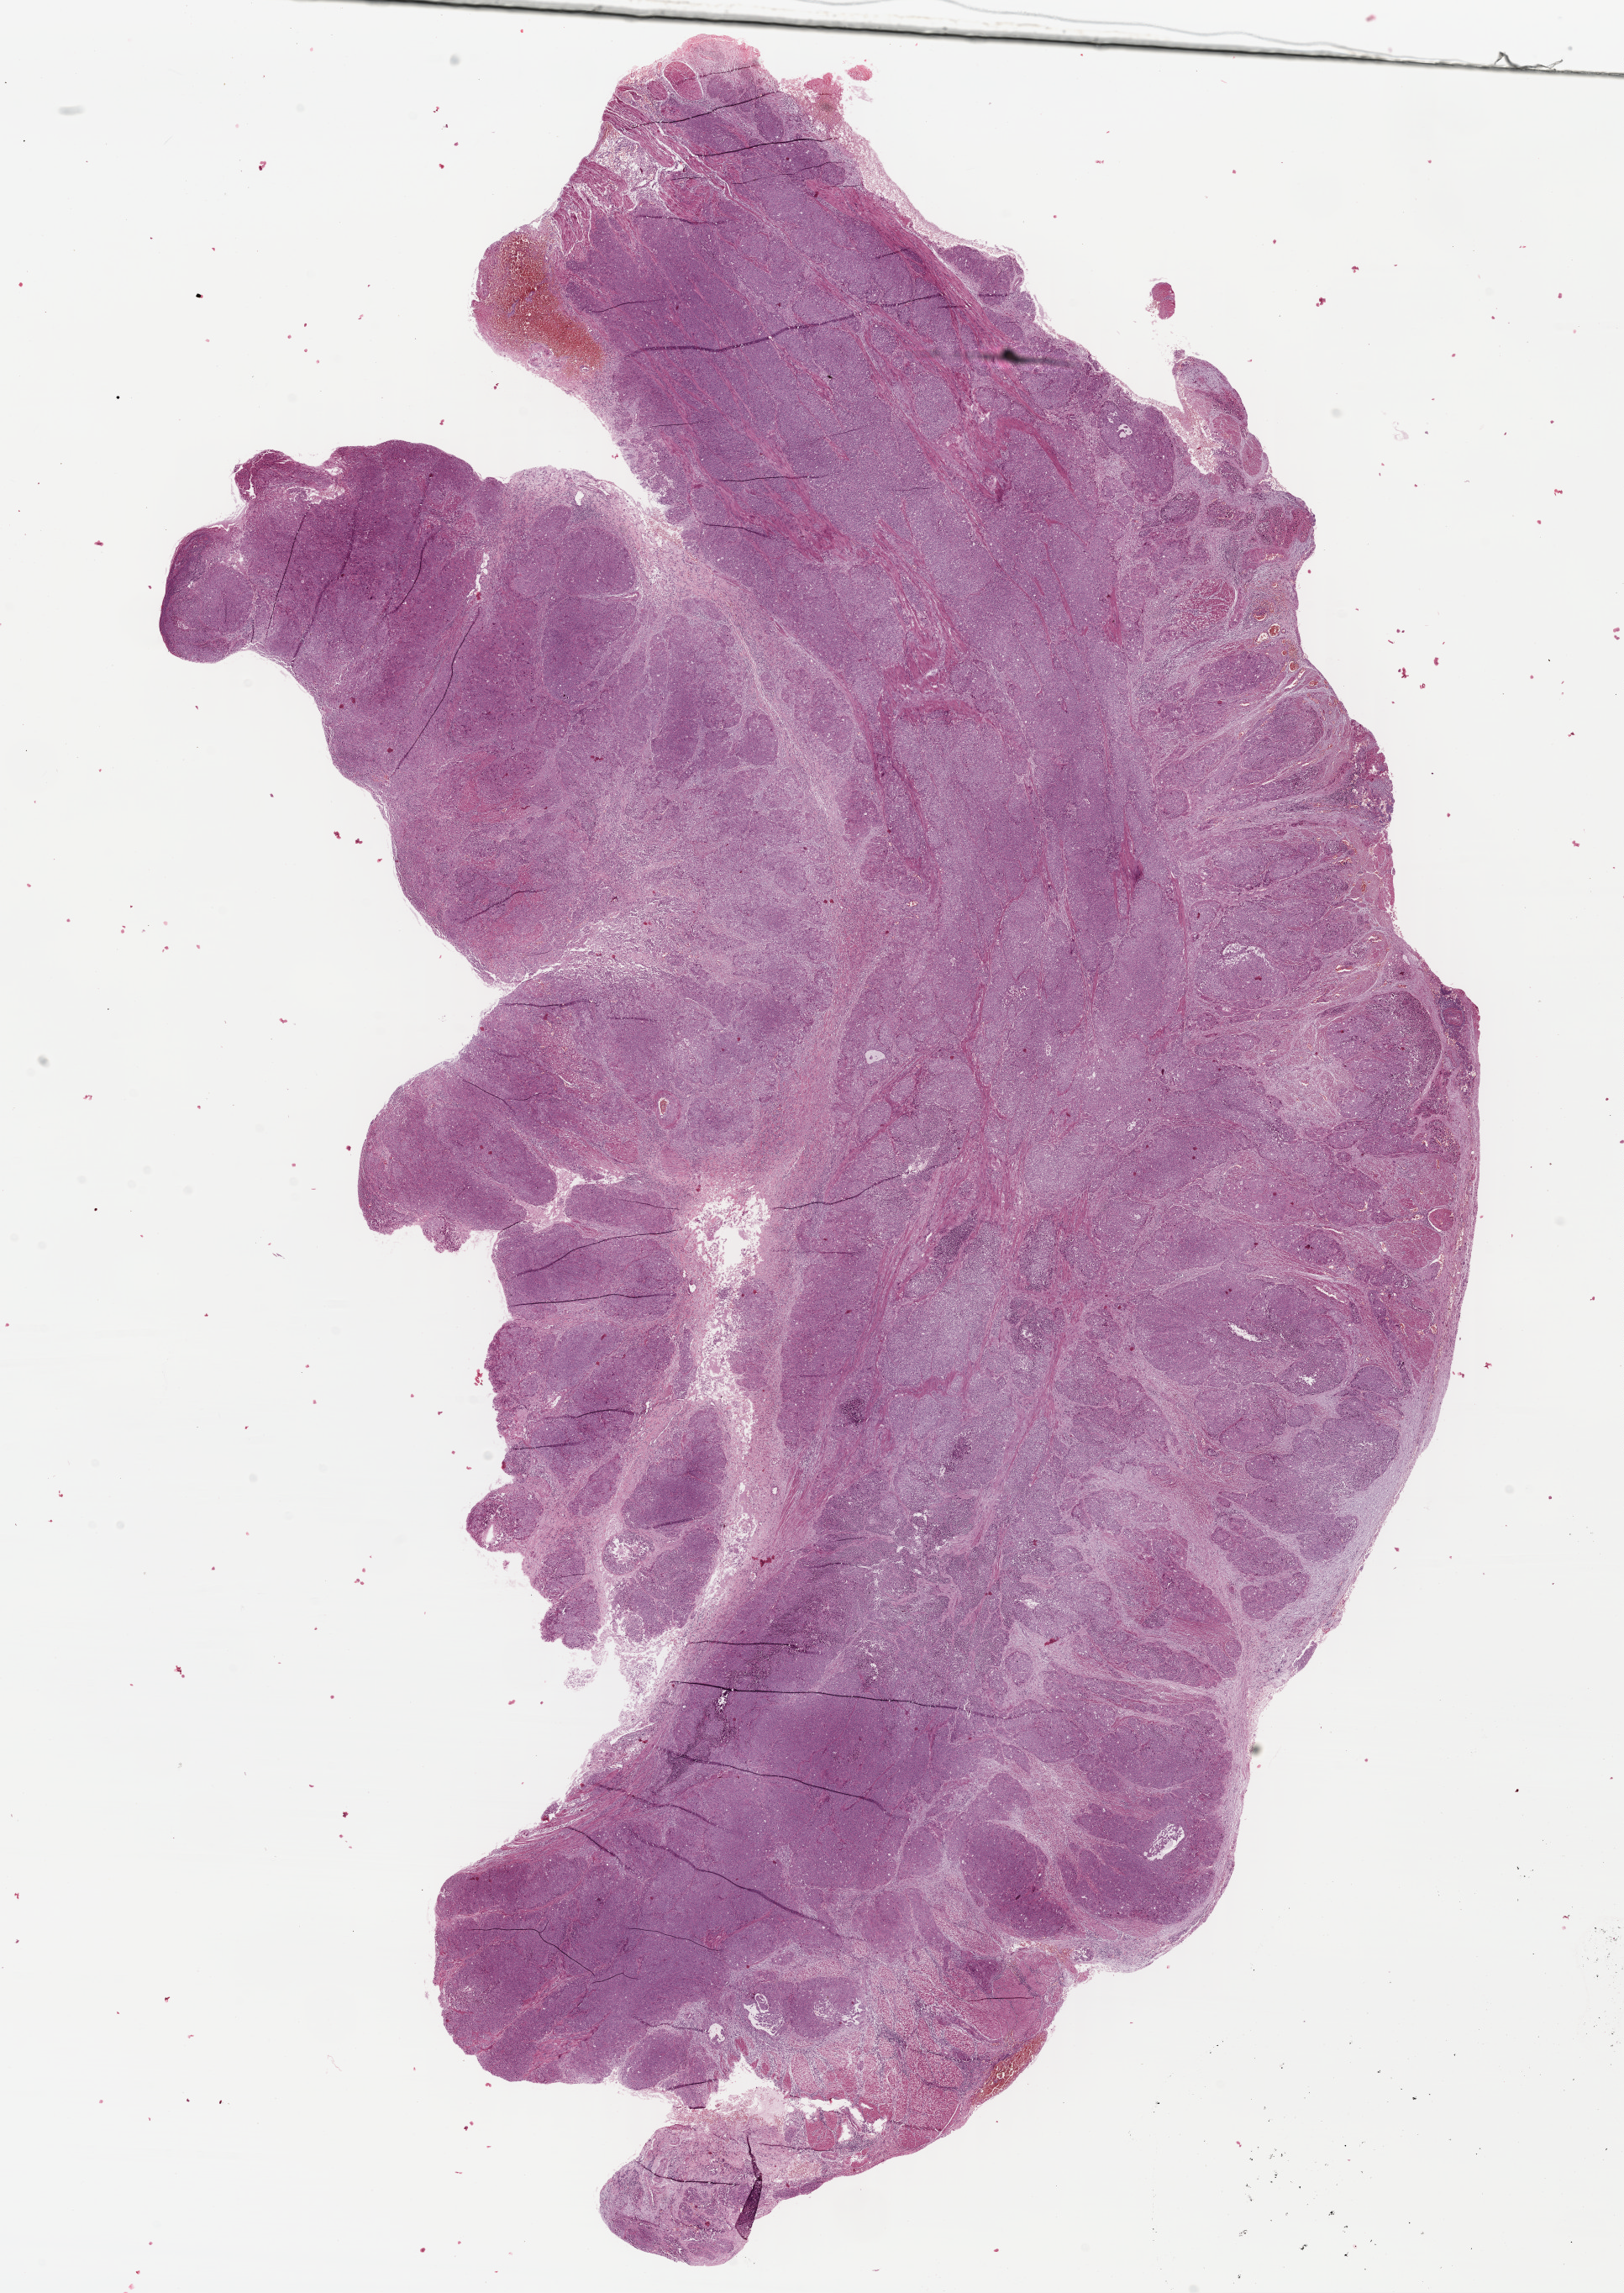
H&E-stained whole-slide image, a low-resolution overview of the entire scanned area, about 15.2 x 21.5 mm; formalin-fixed paraffin-embedded (FFPE) diagnostic section; primary tumour sample from the esophagus. Patient: male, age at initial diagnosis 57 years.
Pathologic diagnosis: Squamous cell carcinoma, NOS.